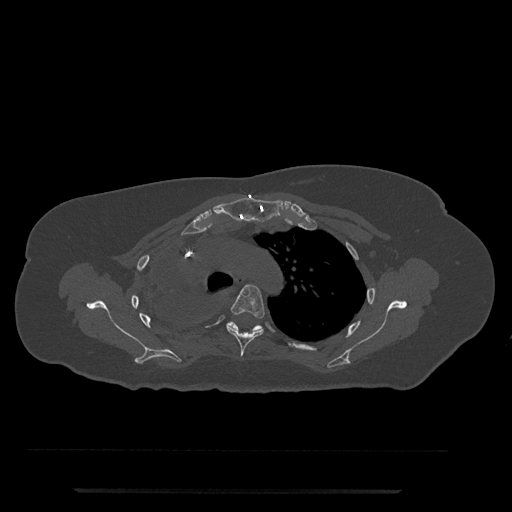
CT including the spine, one axial slice. Slice 578 of 797 in the series (ordered by position). Reconstruction kernel Br40s/3. Bone window (W 1800 / L 400 HU). 512 × 512 image matrix, field of view 440 × 440 mm. Patient: female, 51 years. From the clinical record (not read from this slice): primary cancer: neuro.
Annotated regions visible in this slice (semi-automatically segmented with operator editing):
- T4 vertebra: bounding box [x1, y1, x2, y2] px = [227, 285, 265, 357]
- T5 vertebra: [226, 321, 264, 333]